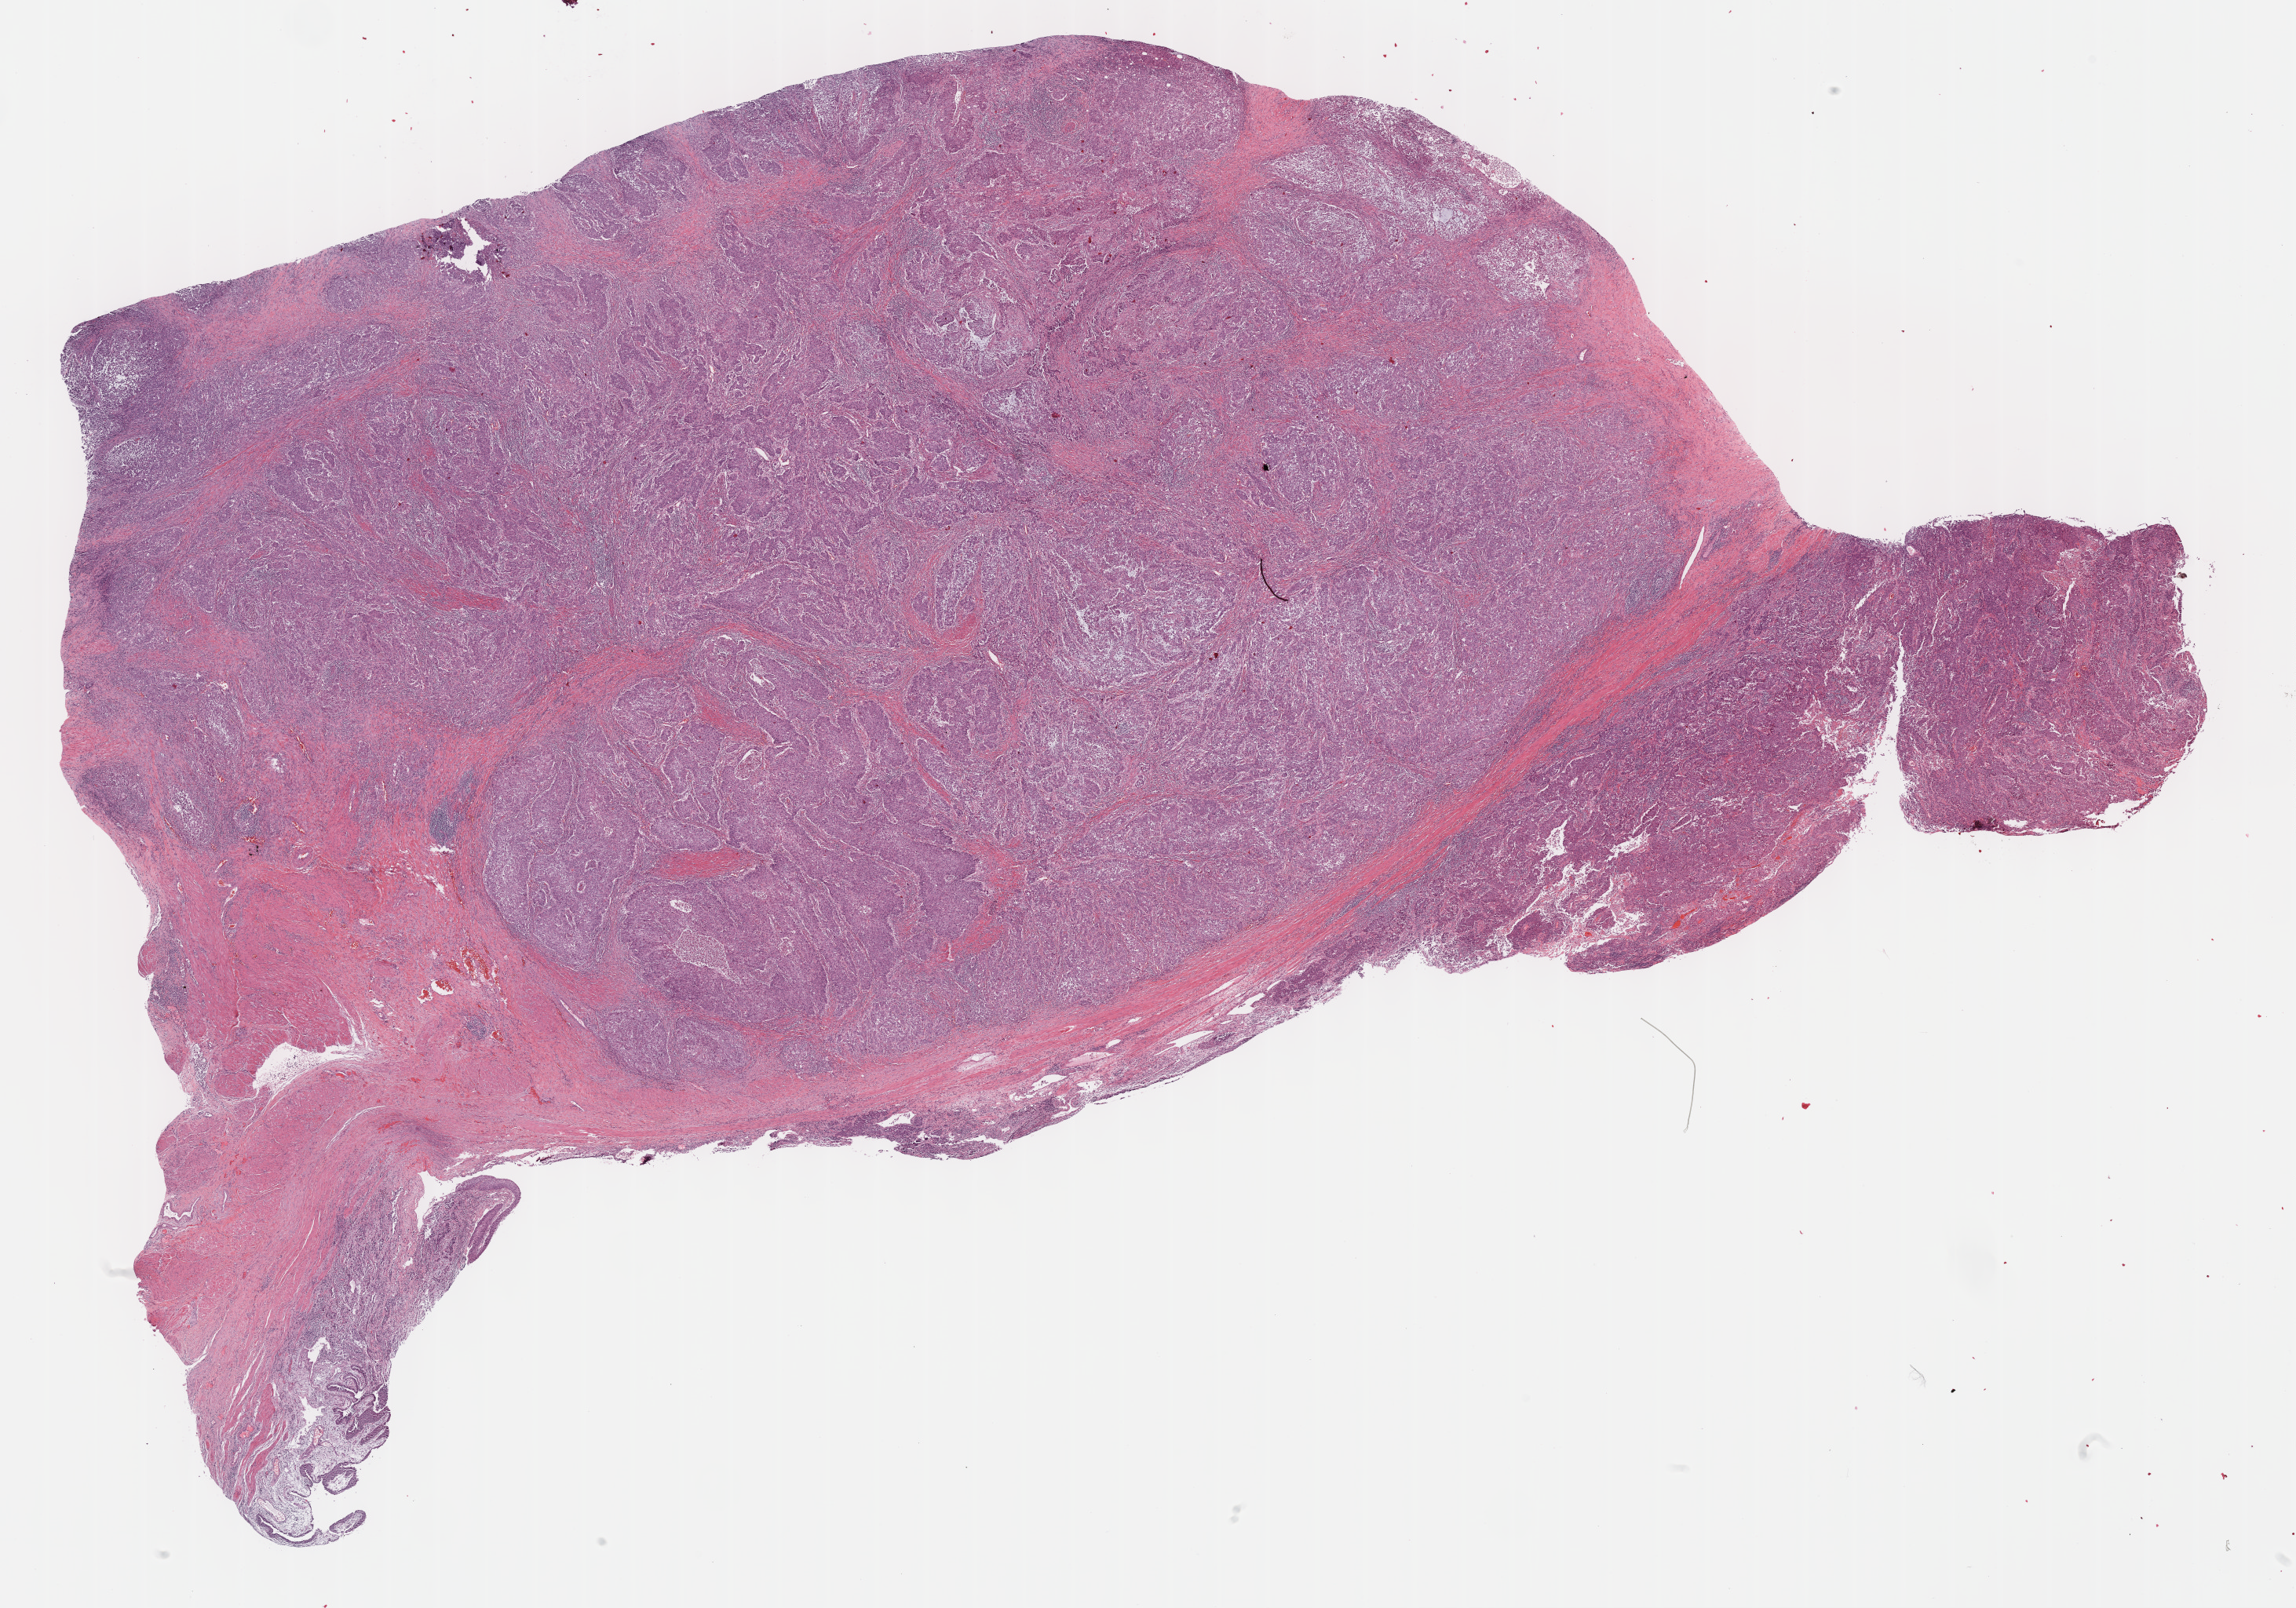
Digitized Hematoxylin and eosin (H&E) stained tissue section (whole slide), low-resolution overview of the scanned area, about 23.7 x 16.6 mm; formalin-fixed paraffin-embedded (FFPE) diagnostic section; primary tumour sample from the bladder. Female patient; age at initial diagnosis 74 years.
Diagnosis: Transitional cell carcinoma.